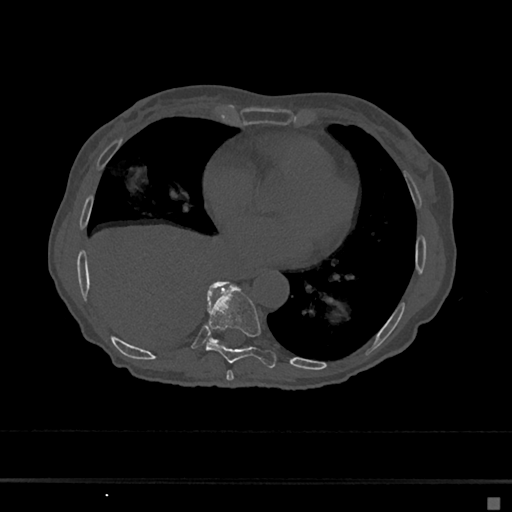
CT including the spine, one axial slice. Slice 316 of 797 in the series (ordered by position). Reconstruction kernel Br40s/3. Bone window (W 1800 / L 400 HU). 0.5 mm slice thickness. 512 × 512 image matrix, field of view 360 × 360 mm. Patient: female, 68 years. Case-level facts recorded for this patient, not image findings: primary cancer: renal.
Structures marked on this image (semi-automatically segmented with operator editing):
- T7 vertebra: bounding box (x1, y1, x2, y2) in pixels: (226, 370, 234, 381)
- T8 vertebra: (205, 282, 276, 368)
- T9 vertebra: (209, 281, 226, 343)